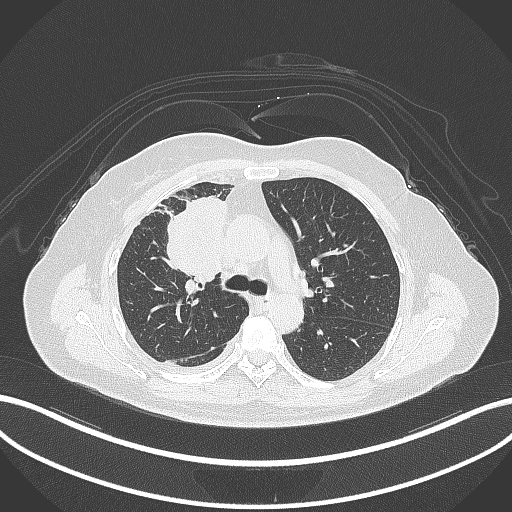
Chest CT, one axial slice. Reconstruction kernel B70f. 120 kVp. Lung window (W 1500 / L -600 HU). 1 mm slice thickness. 512 × 512 image matrix, field of view 400 × 400 mm. Female patient, age 52 years. Case-level facts recorded for this patient, not image findings: clinical TNM (as recorded): T3 N1 M1.
Structures marked on this image (rectangle marked by the reading radiologist):
- lung tumour (recorded histology: adenocarcinoma): bounding box <161,190,228,284> (left, top, right, bottom; pixels)